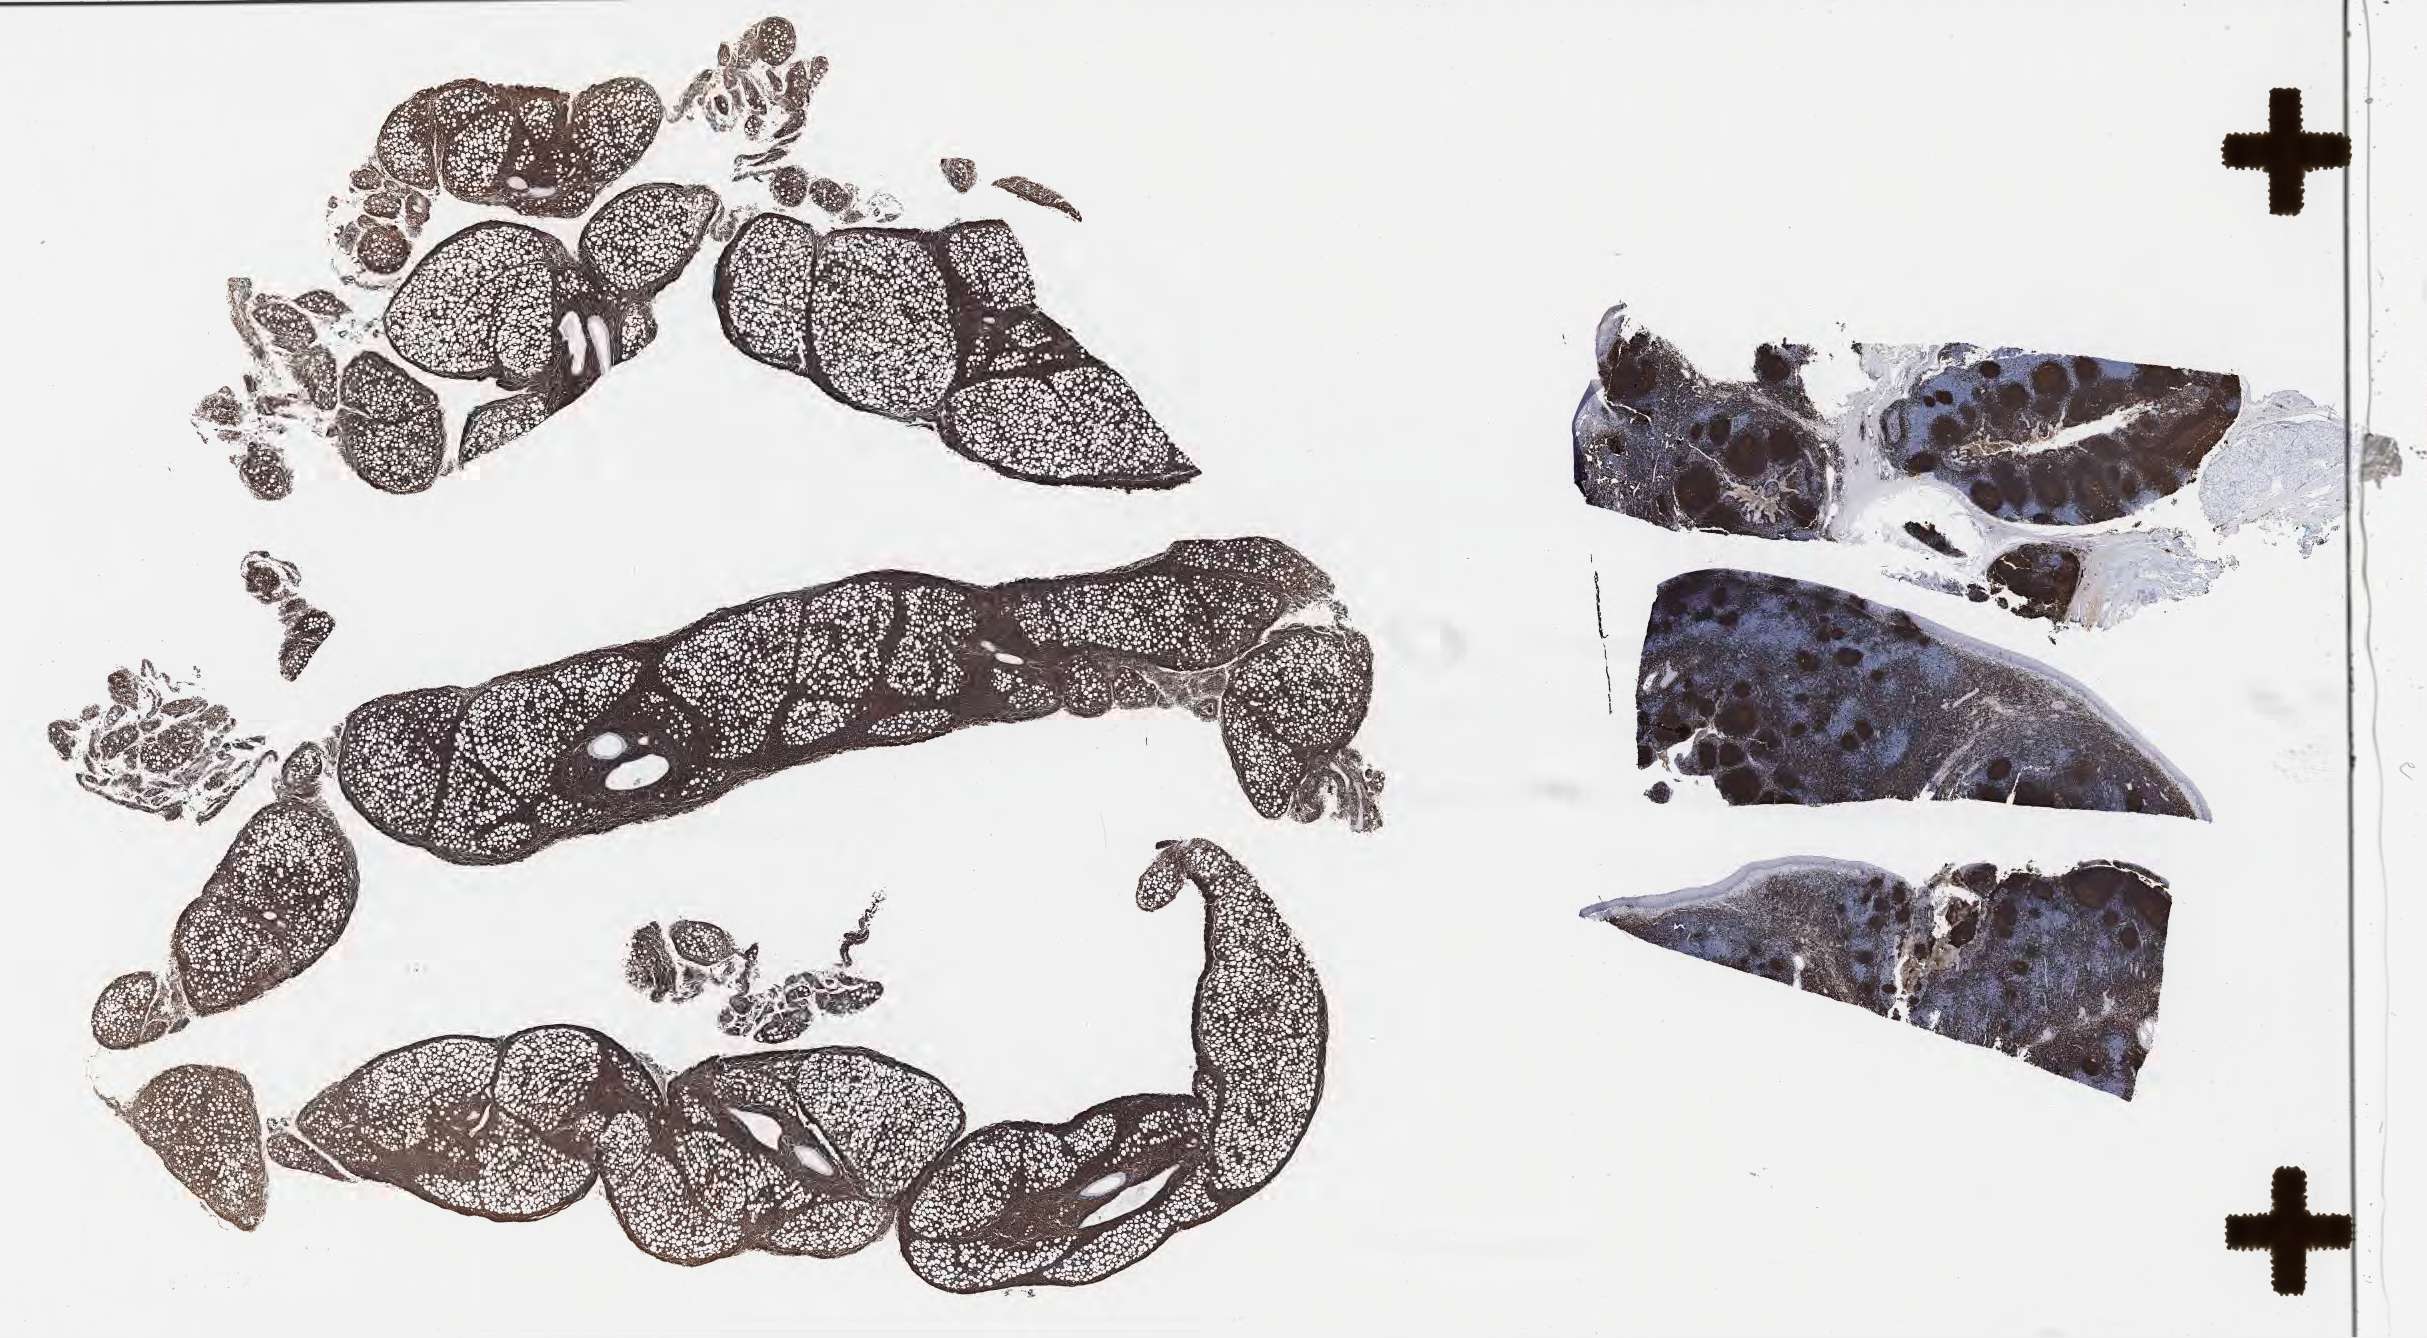
Immunohistochemistry (IHC) whole-slide image stained for CD20, a low-resolution overview of the entire scanned area, about 39.3 x 21.6 mm, tumor tissue, site: abdomen proper. Patient: female, age at initial diagnosis 9 years.
- histologic diagnosis: Burkitt lymphoma, NOS